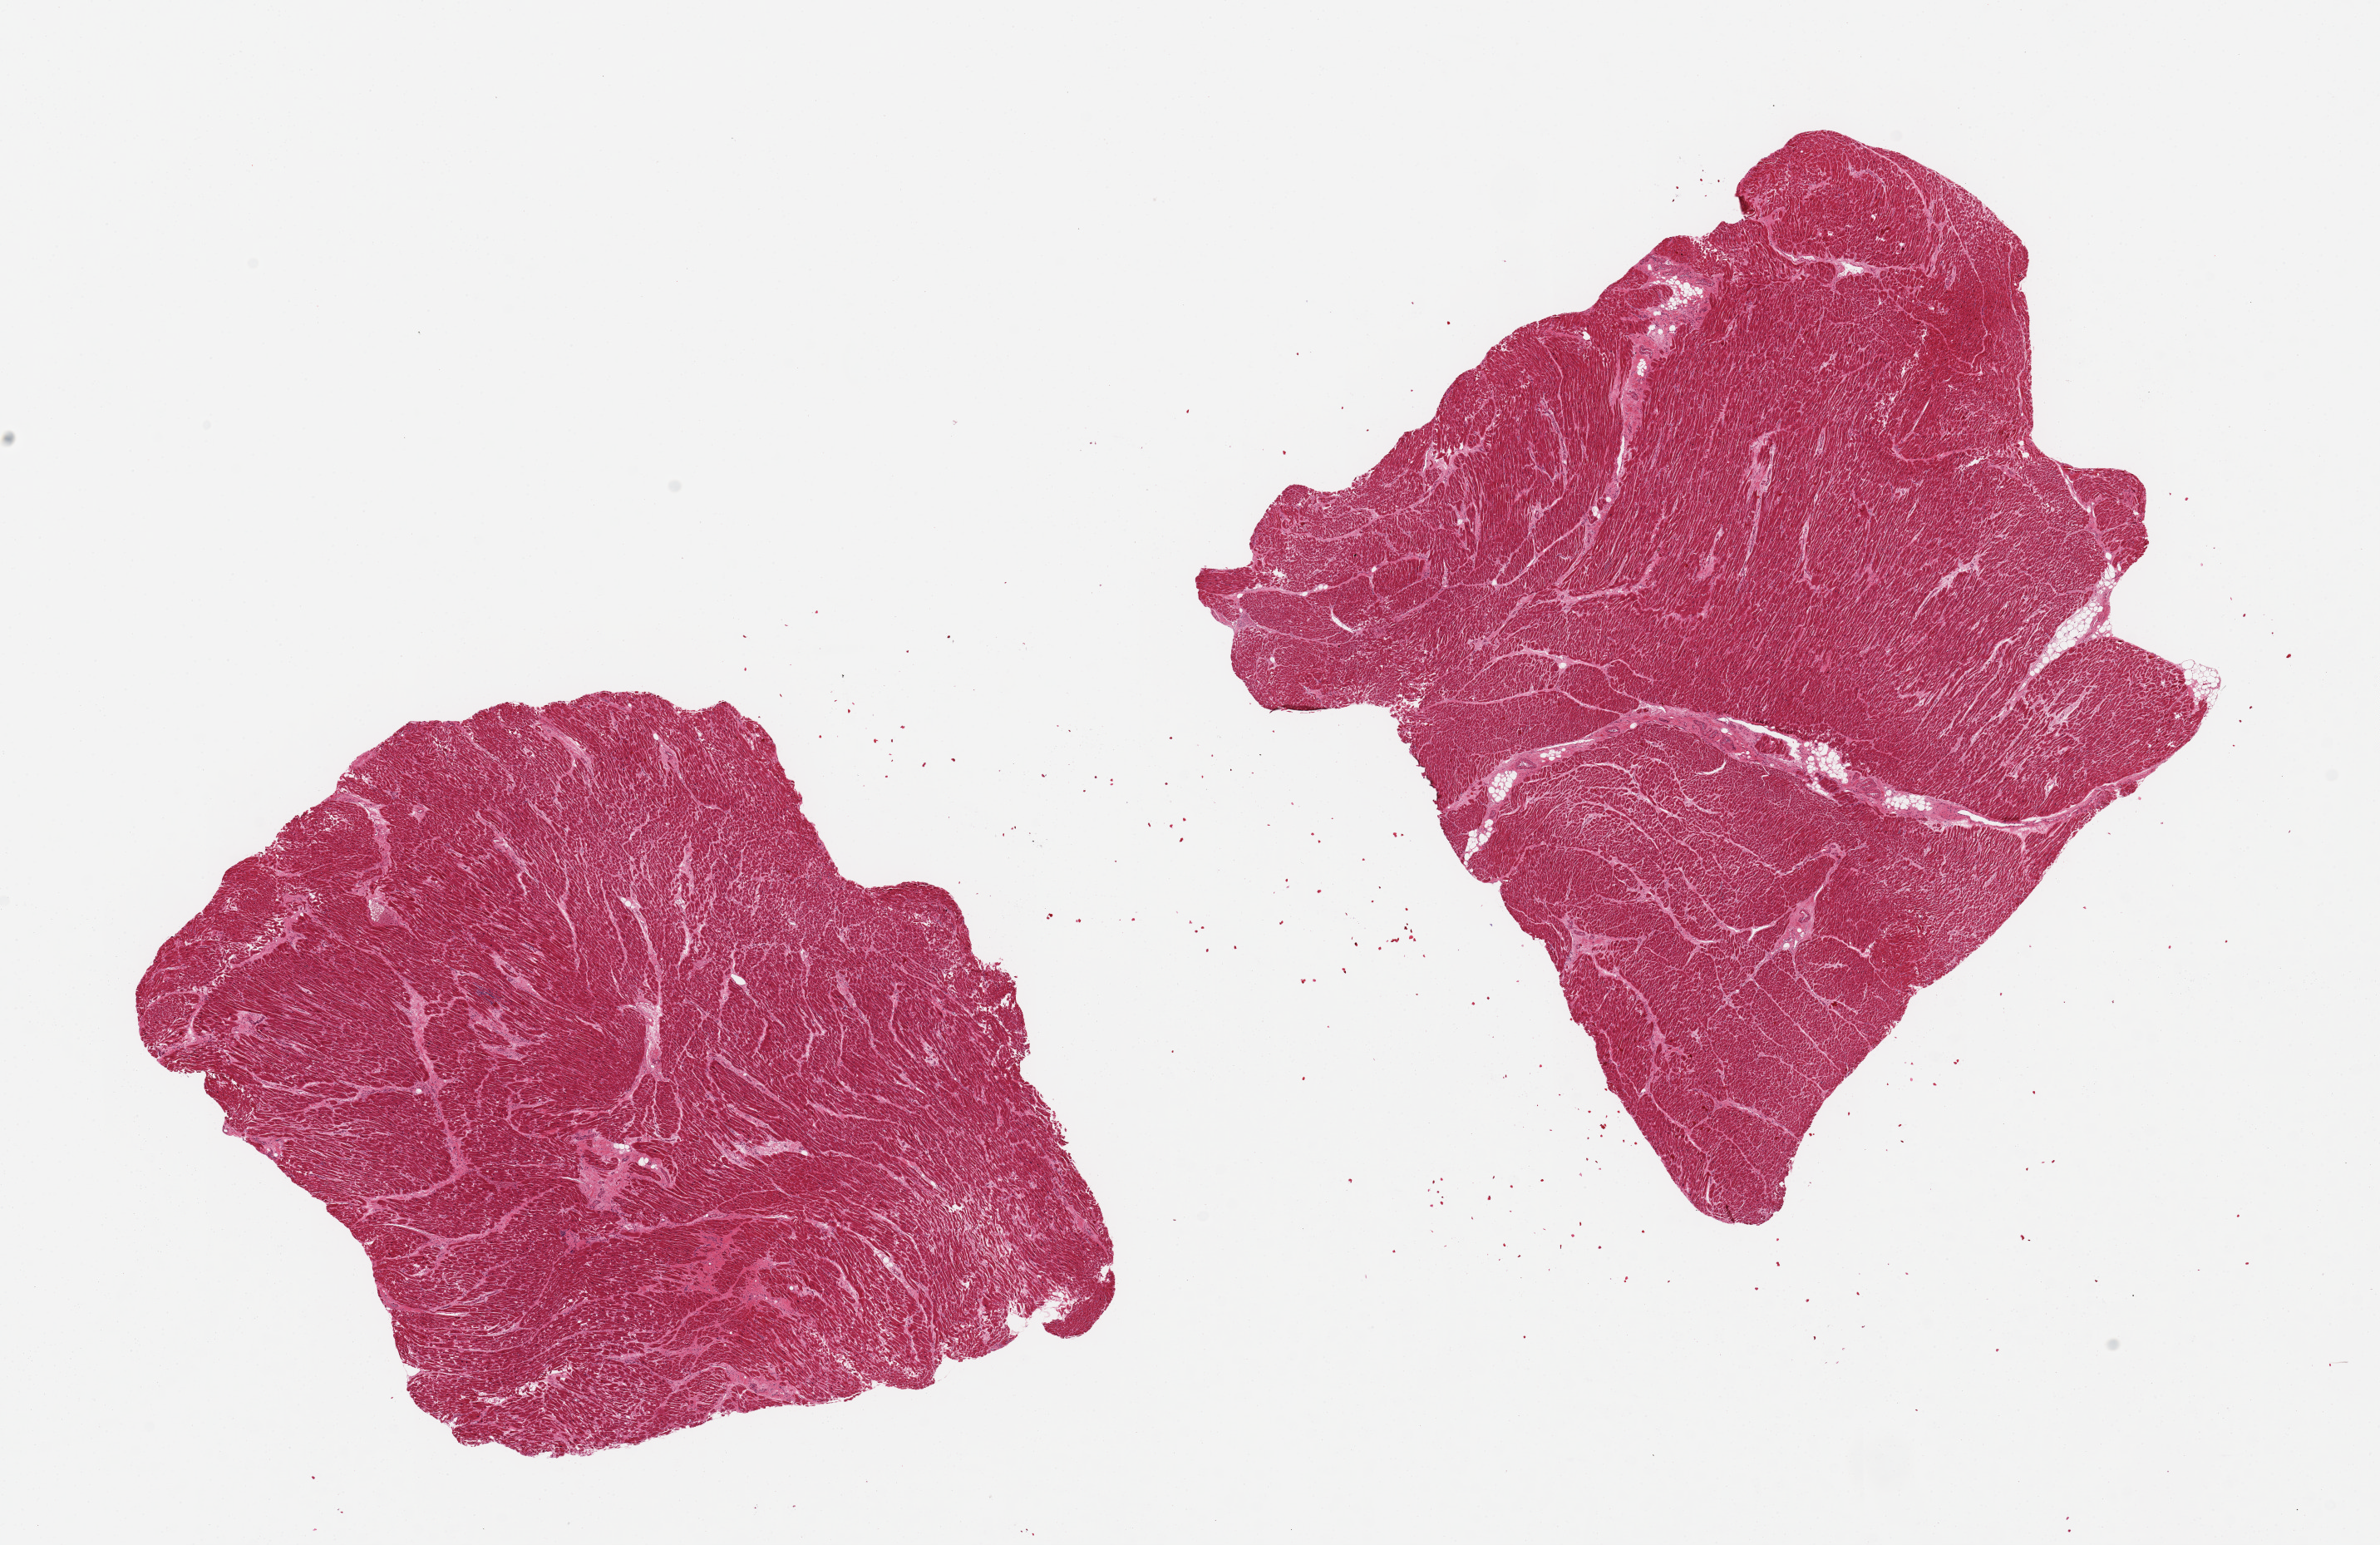
Digitized hematoxylin and eosin (H&E)-stained section, whole scanned area (about 22.6 x 14.7 mm) shown as a low-resolution overview. PAXgene-fixed paraffin-embedded (PFPE) section. Target tissue: heart. Donor tissue sample. Donor sex: male.
Review note (as recorded): 2 pieces, chronic/subacute ischemic changes, microinfract.